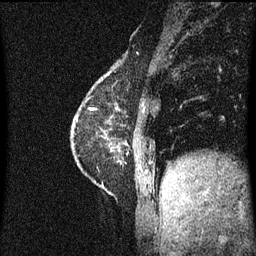
Breast MRI (dynamic contrast-enhanced), one sagittal slice; position 15 of 60 along the scan axis; dynamic contrast-enhanced series, image 2 of 3 at this slice position (ordered by acquisition); 1.5 T; TE 4.2 ms, TR 8.4 ms; 256 × 256 image matrix, field of view 200 × 200 mm. Patient: female, 60 years.
Annotated regions visible in this slice (semi-automatic segmentation, software-assisted and operator-edited):
- analysis volume of interest (the breast-tissue region the enhancement analysis was run in; not a lesion): bounding box (x1, y1, x2, y2) in pixels: (69, 68, 129, 193)
- tumour enhancement mask (voxels above the 70 % enhancement threshold inside the analysis volume of interest): (99, 72, 128, 151)